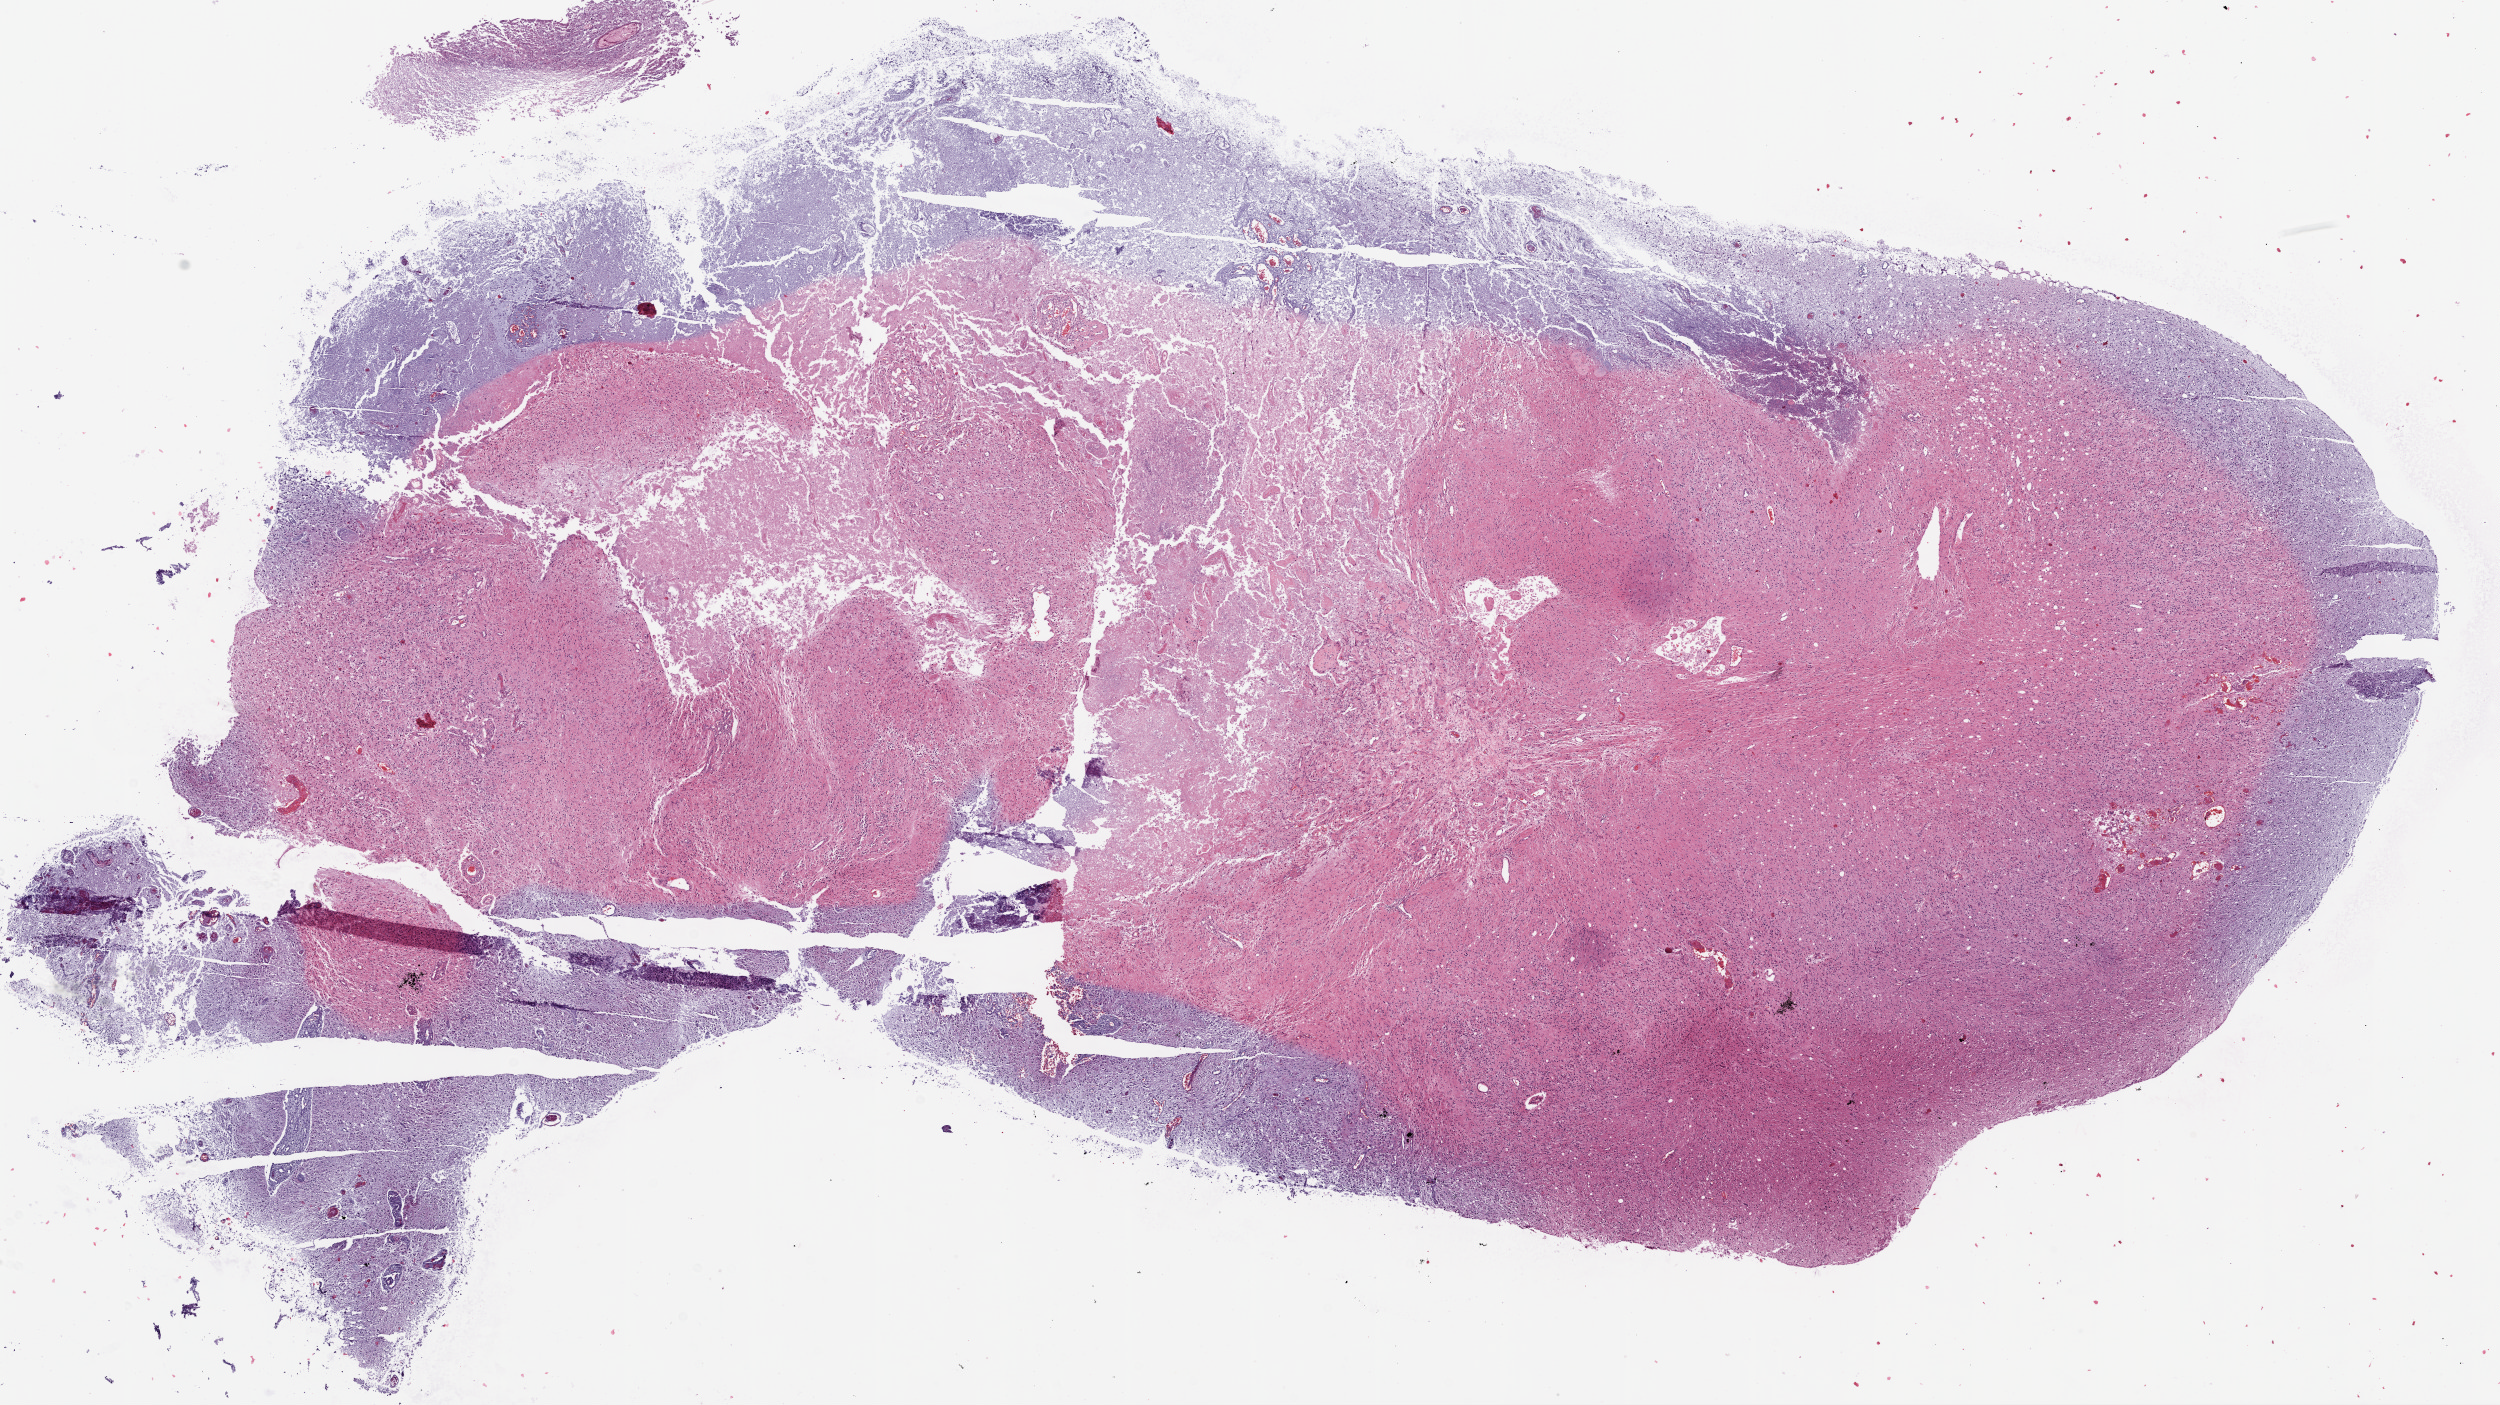
Hematoxylin and eosin (H&E) stained whole-slide image, low-resolution overview of the scanned area, about 20.1 x 11.3 mm (acquisition: 20x scan); formalin-fixed paraffin-embedded (FFPE) diagnostic section; brain, primary tumour sample. Female, age 70 years at initial diagnosis.
Histologic diagnosis: Glioblastoma.